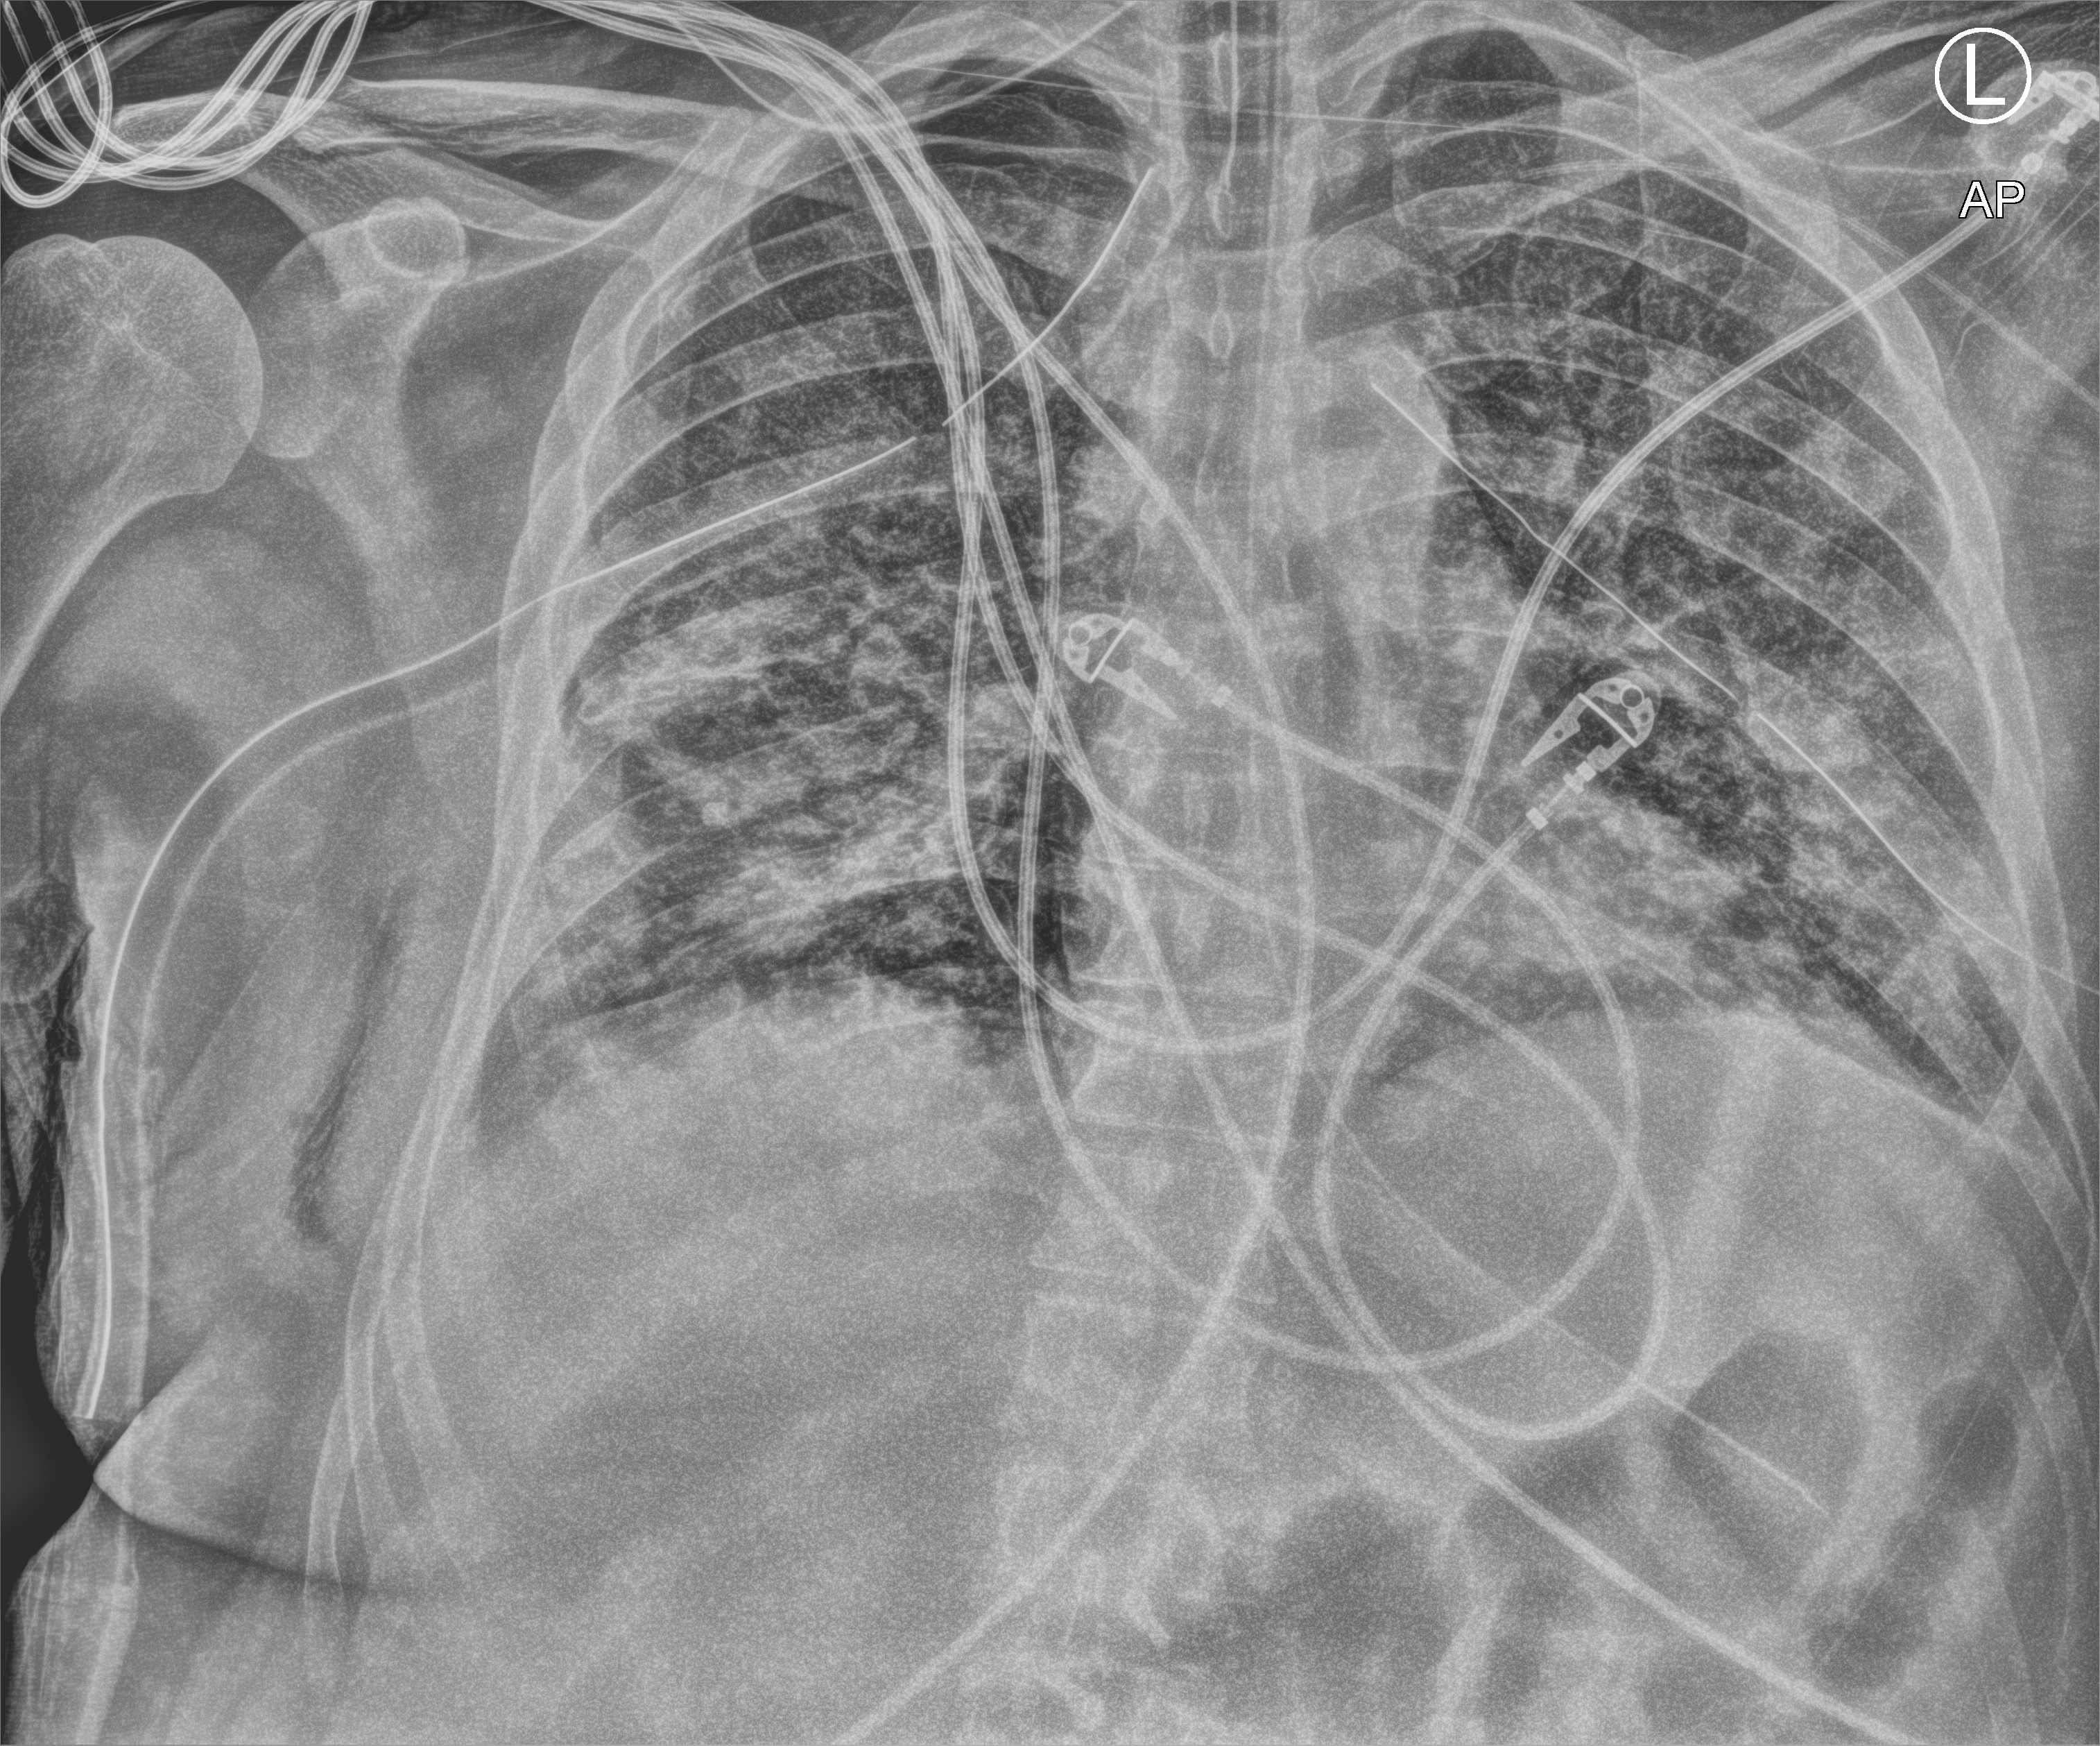
Bedside chest radiograph (computed radiography), anteroposterior (AP) projection. Patient hospitalised with COVID-19; male, aged 18–59 years.
Hospital-stay facts (about this admission, not read from this image; timing relative to this image not recorded):
- mechanically ventilated during this hospital stay: yes
- admitted to intensive care during this hospital stay: yes
- length of hospital stay: 63 days